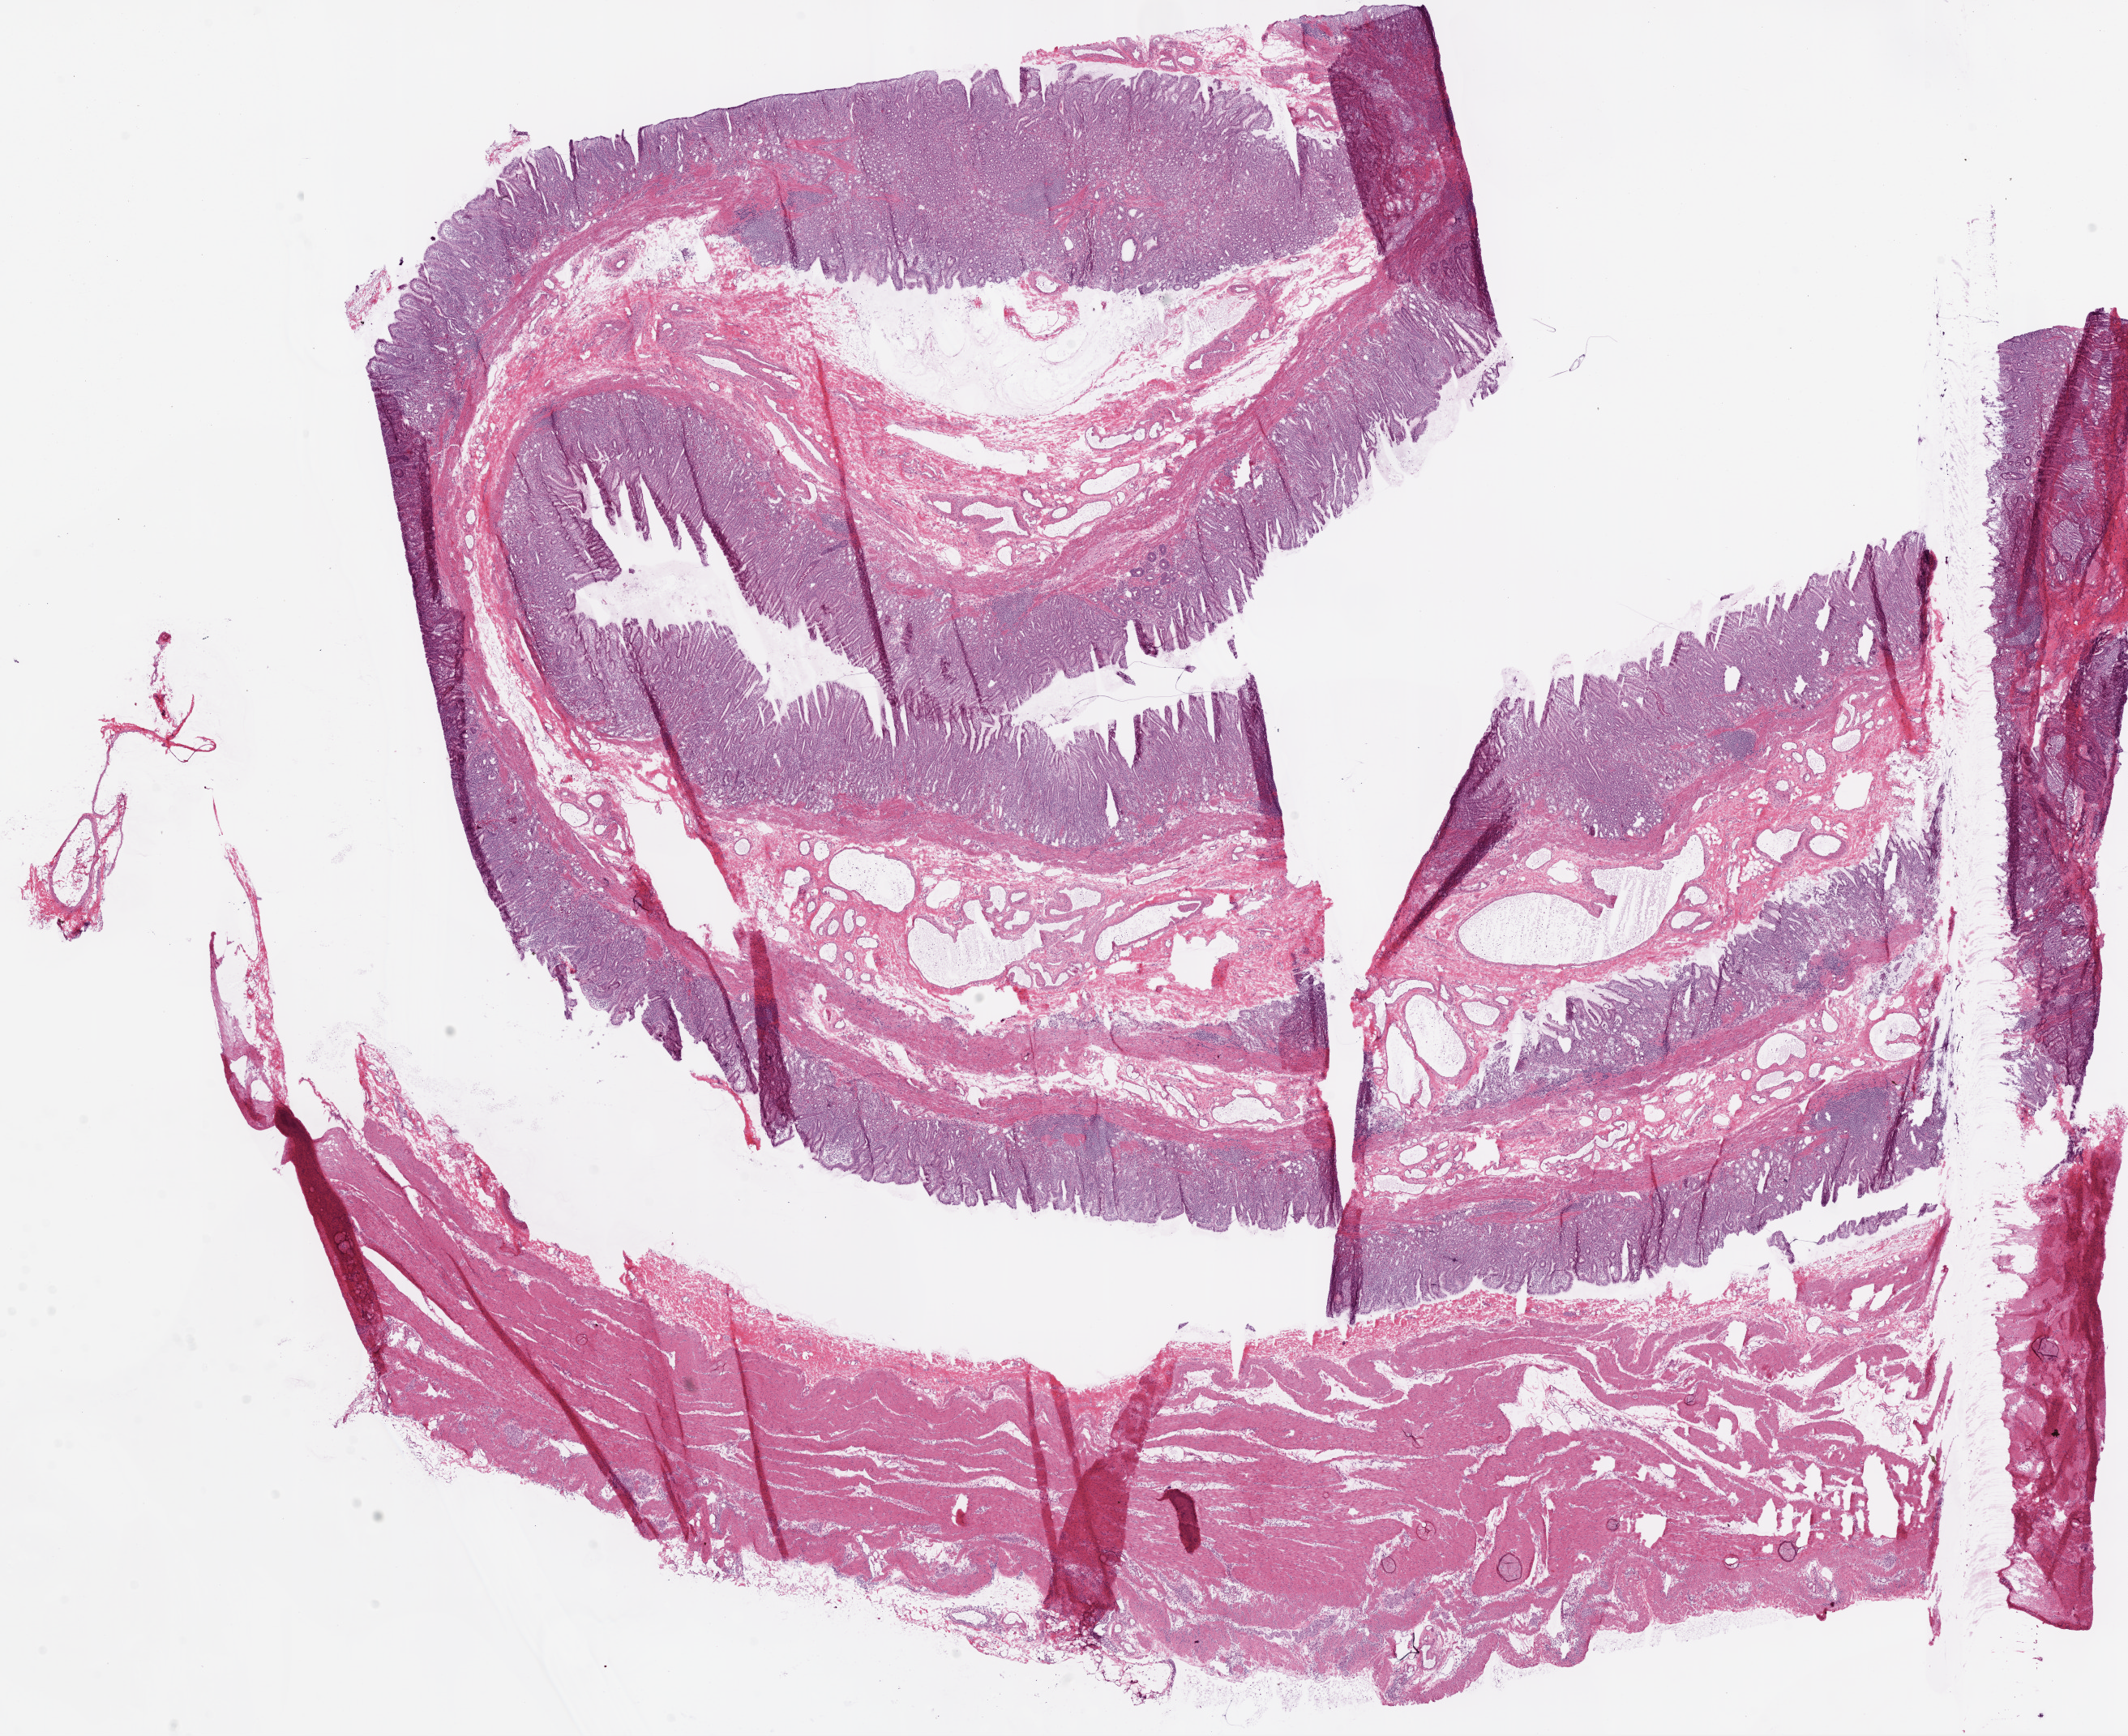
Digitized H&E tissue section (whole slide), low-resolution overview of the scanned area, about 21.1 x 17.2 mm (slide scanned at 20x). Frozen section from the bottom of the tissue portion. Stomach, solid tissue normal (non-tumour tissue) sample. Male patient; age at initial diagnosis 72 years.
• this section: solid tissue normal sample (biorepository sample class)
• patient diagnosis: Adenocarcinoma, NOS